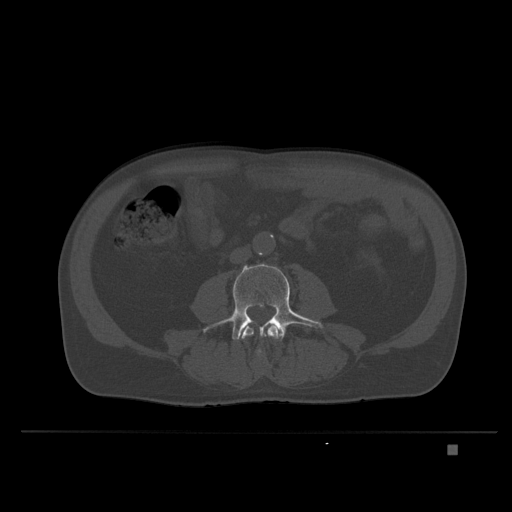
CT including the spine, one axial slice. Position 81 of 435 along the scan axis. Bone window (W 1800 / L 400 HU). 512 × 512 image matrix, field of view 434 × 434 mm. Patient: male, 73 years. From the clinical record (not read from this slice): primary cancer: skin.
Outlined on this slice (semi-automatically segmented with operator editing):
- L3 vertebra: bounding box (x1, y1, x2, y2) in pixels: (241, 323, 283, 340)
- L4 vertebra: (203, 263, 324, 363)